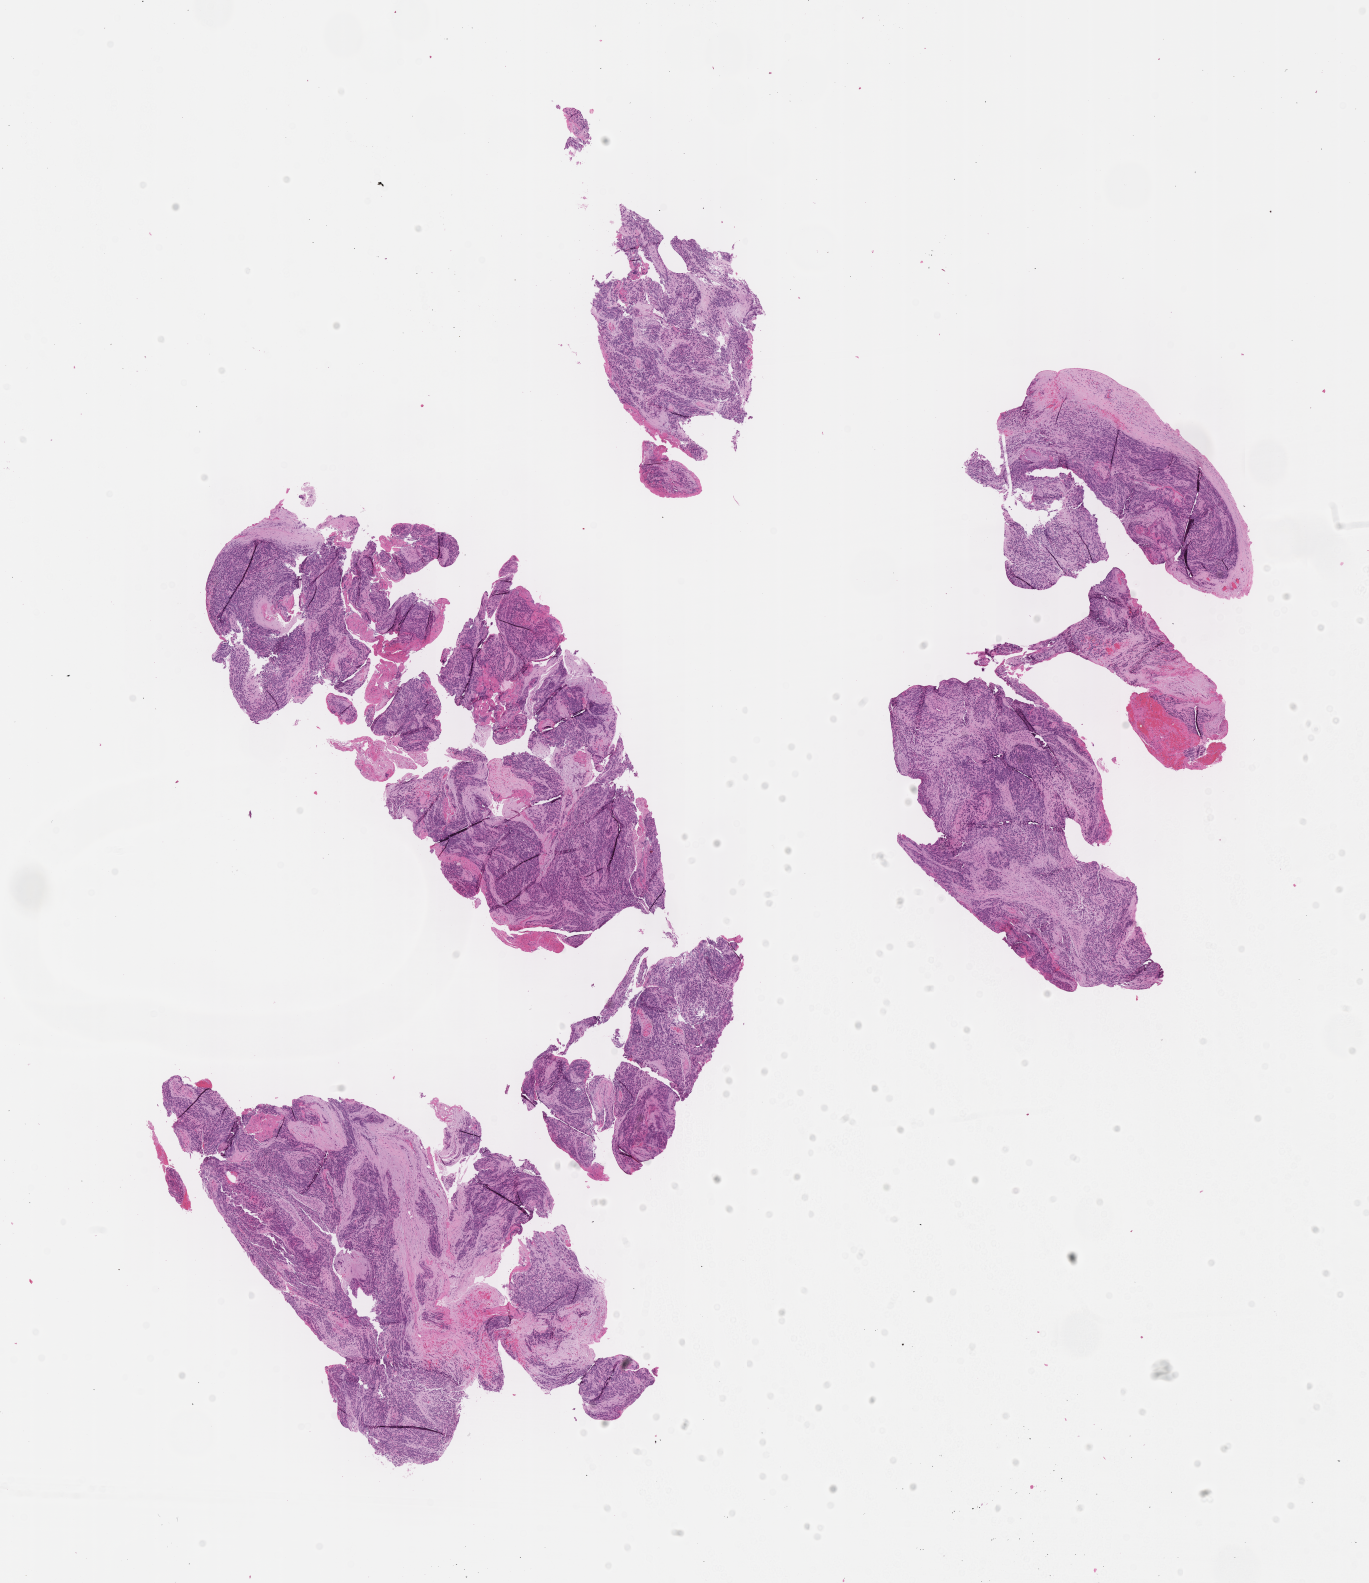
Digitized haematoxylin and eosin-stained section of tumor tissue, shown as a low-resolution overview of the whole scanned area (about 11.1 x 12.8 mm), formalin-fixed paraffin-embedded section, sample anatomic site: eye, orbit-right. Patient: male, age 6.3 years at diagnosis.
Diagnosis: rhabdomyosarcoma; histological classification: embryonal rhabdomyosarcoma. Metastatic status at presentation (as recorded): non-metastatic. Stage (as recorded): 1.